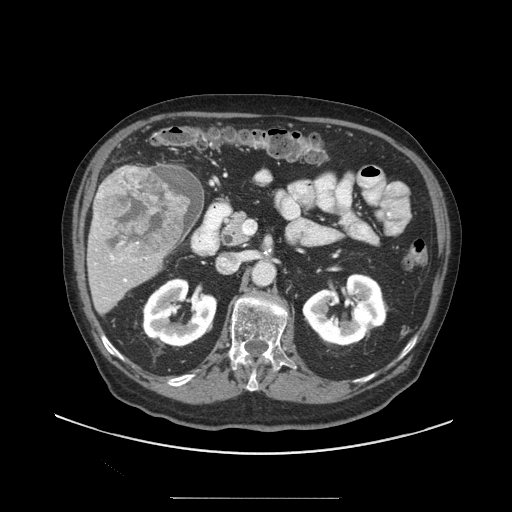
Contrast-enhanced abdominal CT (liver protocol), one axial slice. Reconstruction kernel STANDARD. 140 kVp. Soft-tissue window (W 400 / L 40 HU). 2.5 mm slice thickness. 512 × 512 image matrix. Case-level facts recorded for this patient, not image findings: diagnosis: hepatocellular carcinoma (patient treated with transarterial chemoembolisation; whether this scan precedes or follows treatment is not stated here); TNM stage (as recorded): Stage-IIIC; Child-Pugh class: A; tumour nodularity: uninodular; tumour size: 9.2 cm.
Annotated regions visible in this slice (semi-automatic segmentation, software-assisted and operator-edited):
- liver parenchyma outside the tumour (the mass and vessels are separate outlines, so this box may not span the whole liver): bounding box (x1, y1, x2, y2) in pixels: (88, 164, 200, 314)
- mass: (95, 165, 188, 258)
- liver vessels: (111, 255, 127, 282)